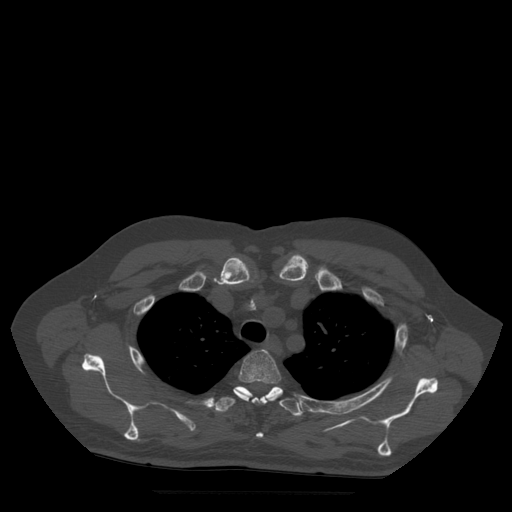
CT including the spine, one axial slice. Position 402 of 522 along the scan axis. Bone window (W 1800 / L 400 HU). 512 × 512 image matrix, field of view 420 × 420 mm. Patient age 72 years. Case-level facts recorded for this patient, not image findings: primary cancer: prostate.
Structures marked on this image (semi-automatic segmentation, software-assisted and operator-edited):
- T3 vertebra: bounding box <233,350,283,438> (left, top, right, bottom; pixels)
- T4 vertebra: <214,386,304,417>